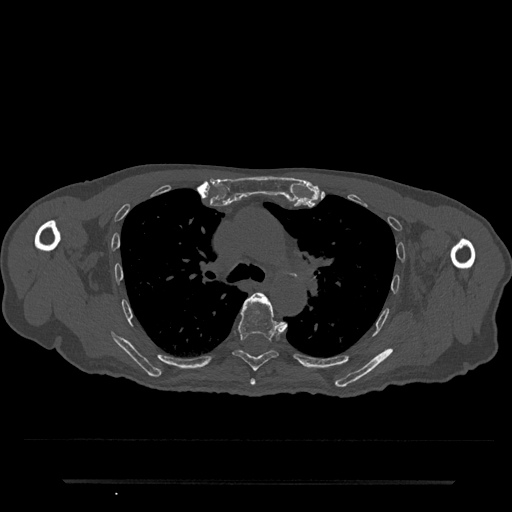
CT including the spine, one axial slice; position 533 of 797 along the scan axis; reconstruction kernel Br40s/3; bone window (W 1800 / L 400 HU); 512 × 512 image matrix, field of view 427 × 427 mm. Male patient, age 74 years. Case-level facts recorded for this patient, not image findings: primary cancer: prostate.
Structures marked on this image (semi-automatic segmentation, software-assisted and operator-edited):
- T5 vertebra: bounding box <250,301,286,386> (left, top, right, bottom; pixels)
- T6 vertebra: <233,292,282,371>